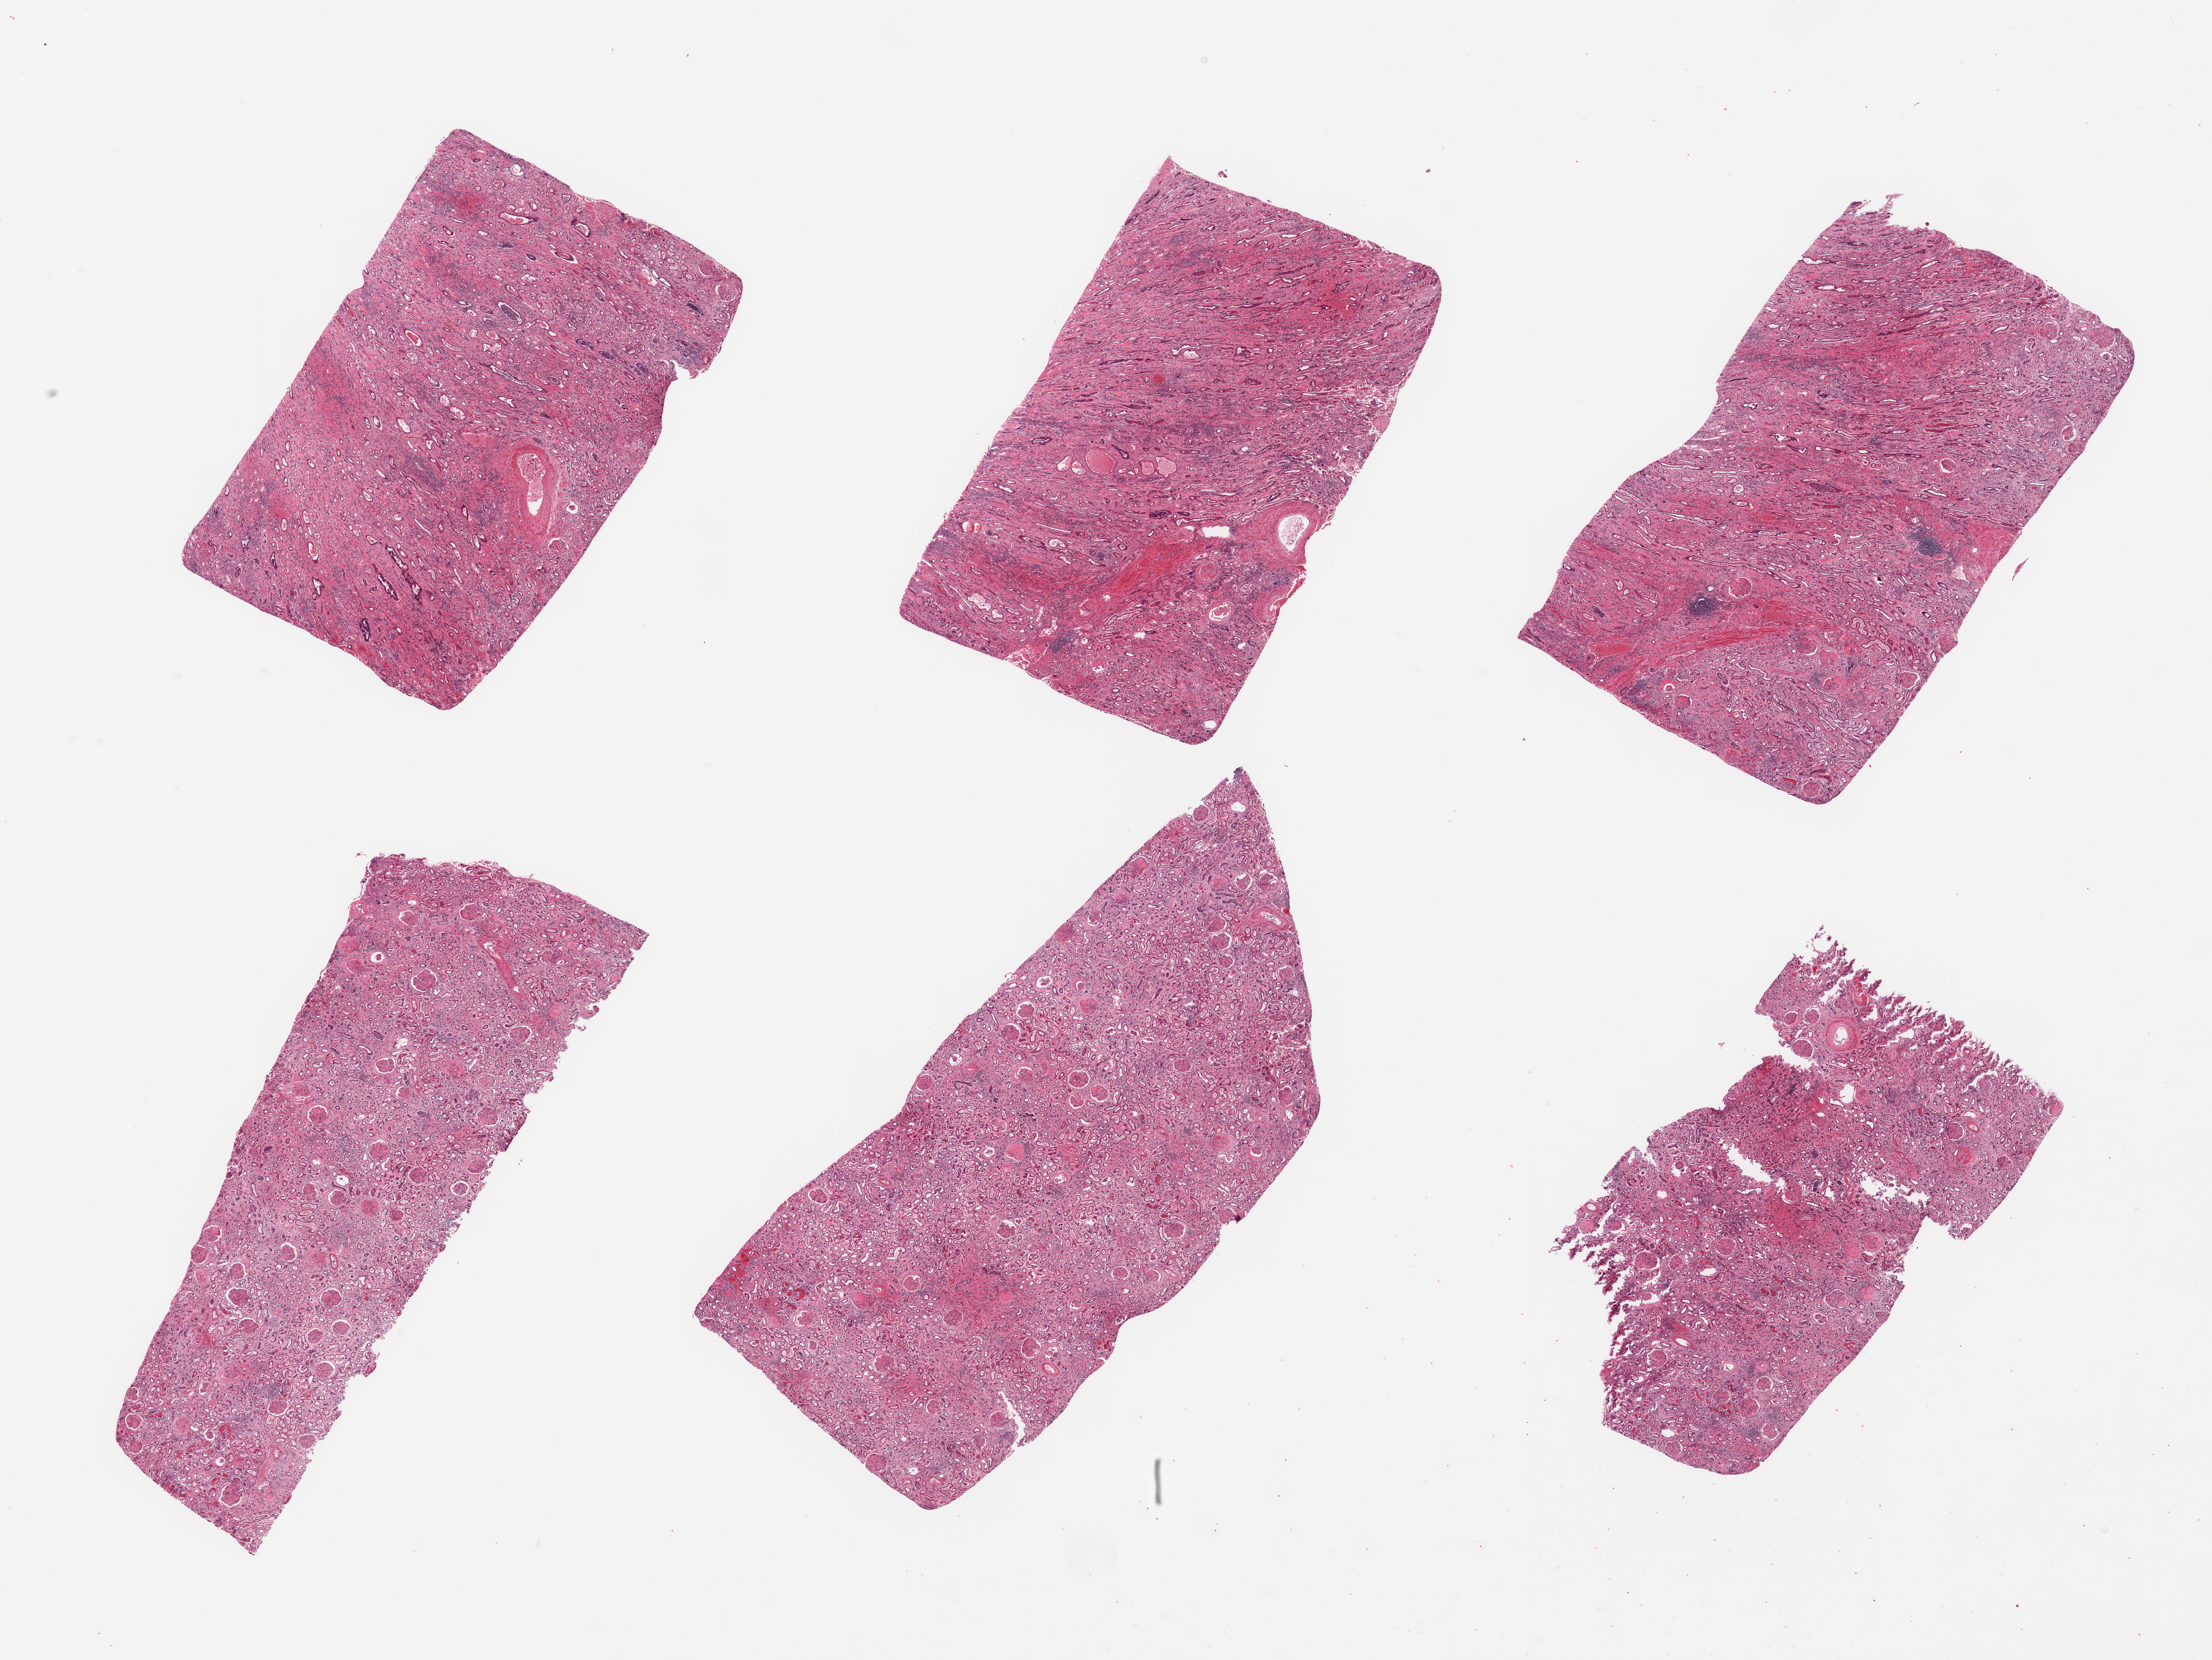
Digitized haematoxylin and eosin-stained section, brightfield — shown as a low-resolution overview of the whole scanned area (about 25.6 x 19.2 mm), PAXgene-fixed, paraffin-embedded tissue, sampled site (target tissue): renal cortex, tissue donor sample.
• pathologist's review note for this sample: 6 pieces; arterio and arteriolo nephrosclerosis; nodular mesangial sclerosis consistent with diabetic nephropathy; congestion and interstitial fibrosis with chronic inflammation; thick tubular basement membranes and some tubules containing acute and chronic inflammatory cells